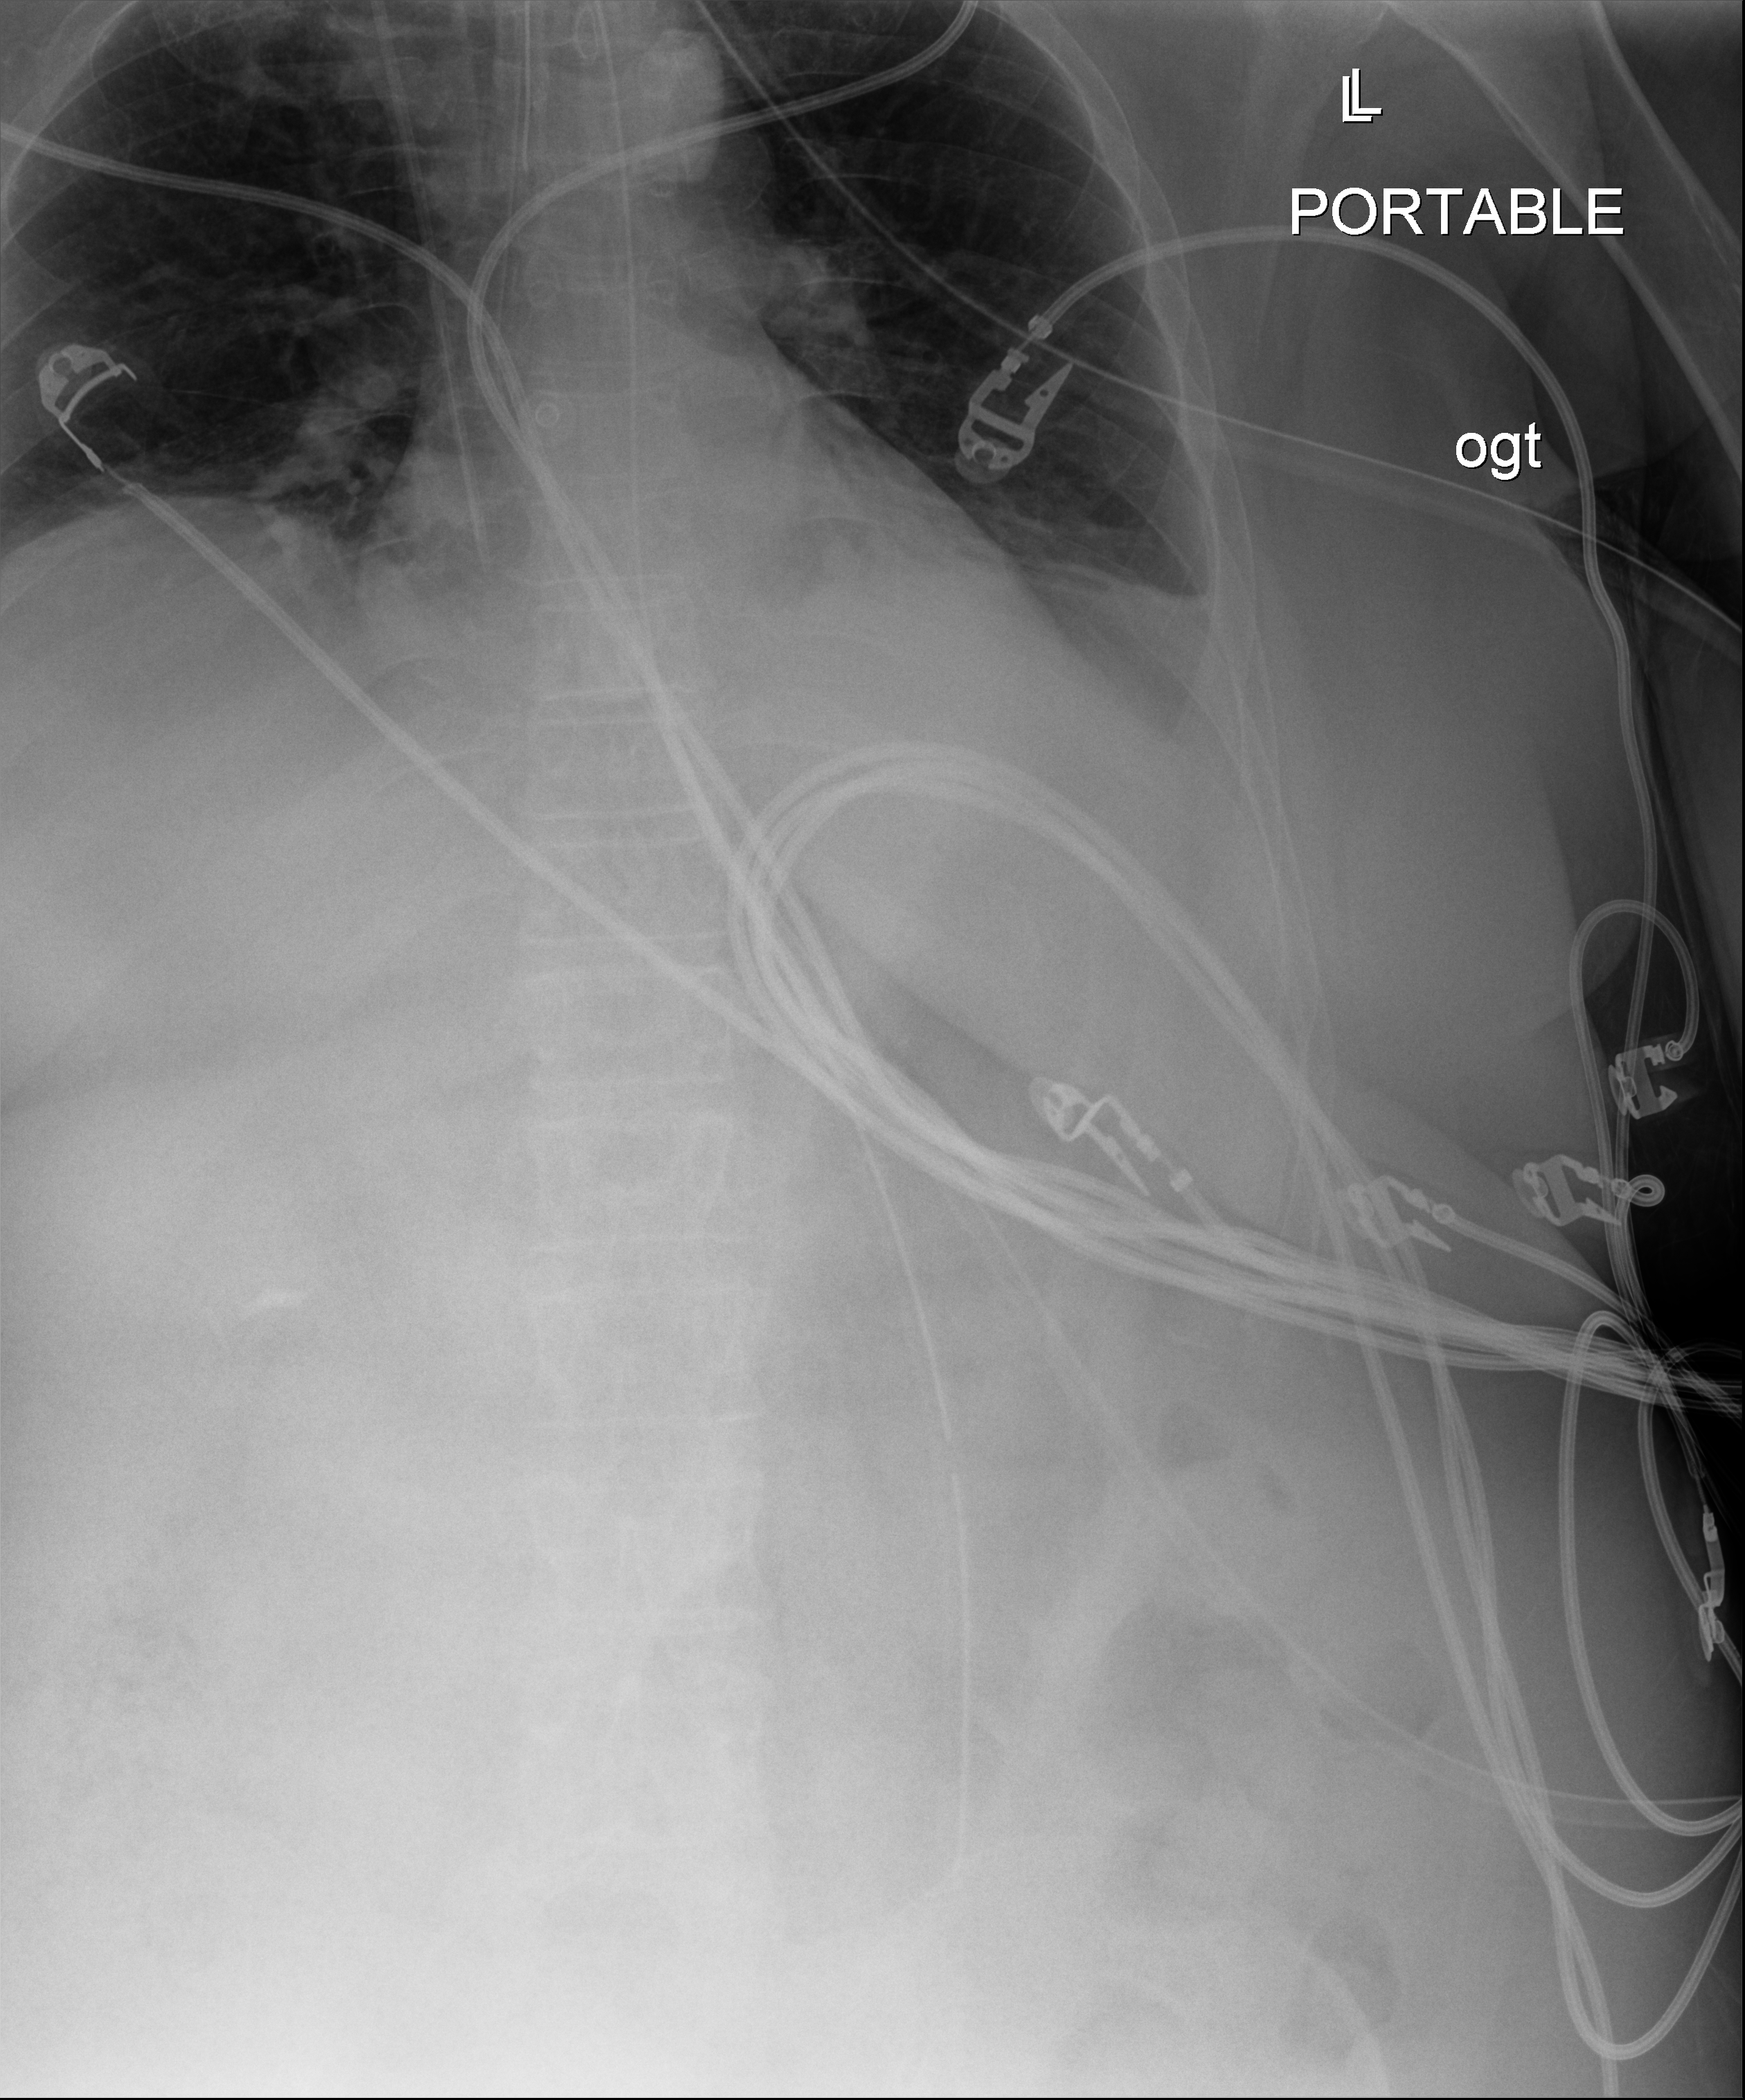
Chest X-ray (portable), anteroposterior (AP) projection. Female patient hospitalised with COVID-19, age 18–59 years.
Hospital-stay facts (about this admission, not read from this image; timing relative to this image not recorded): admitted to intensive care during this hospital stay: yes; mechanically ventilated during this hospital stay: no.